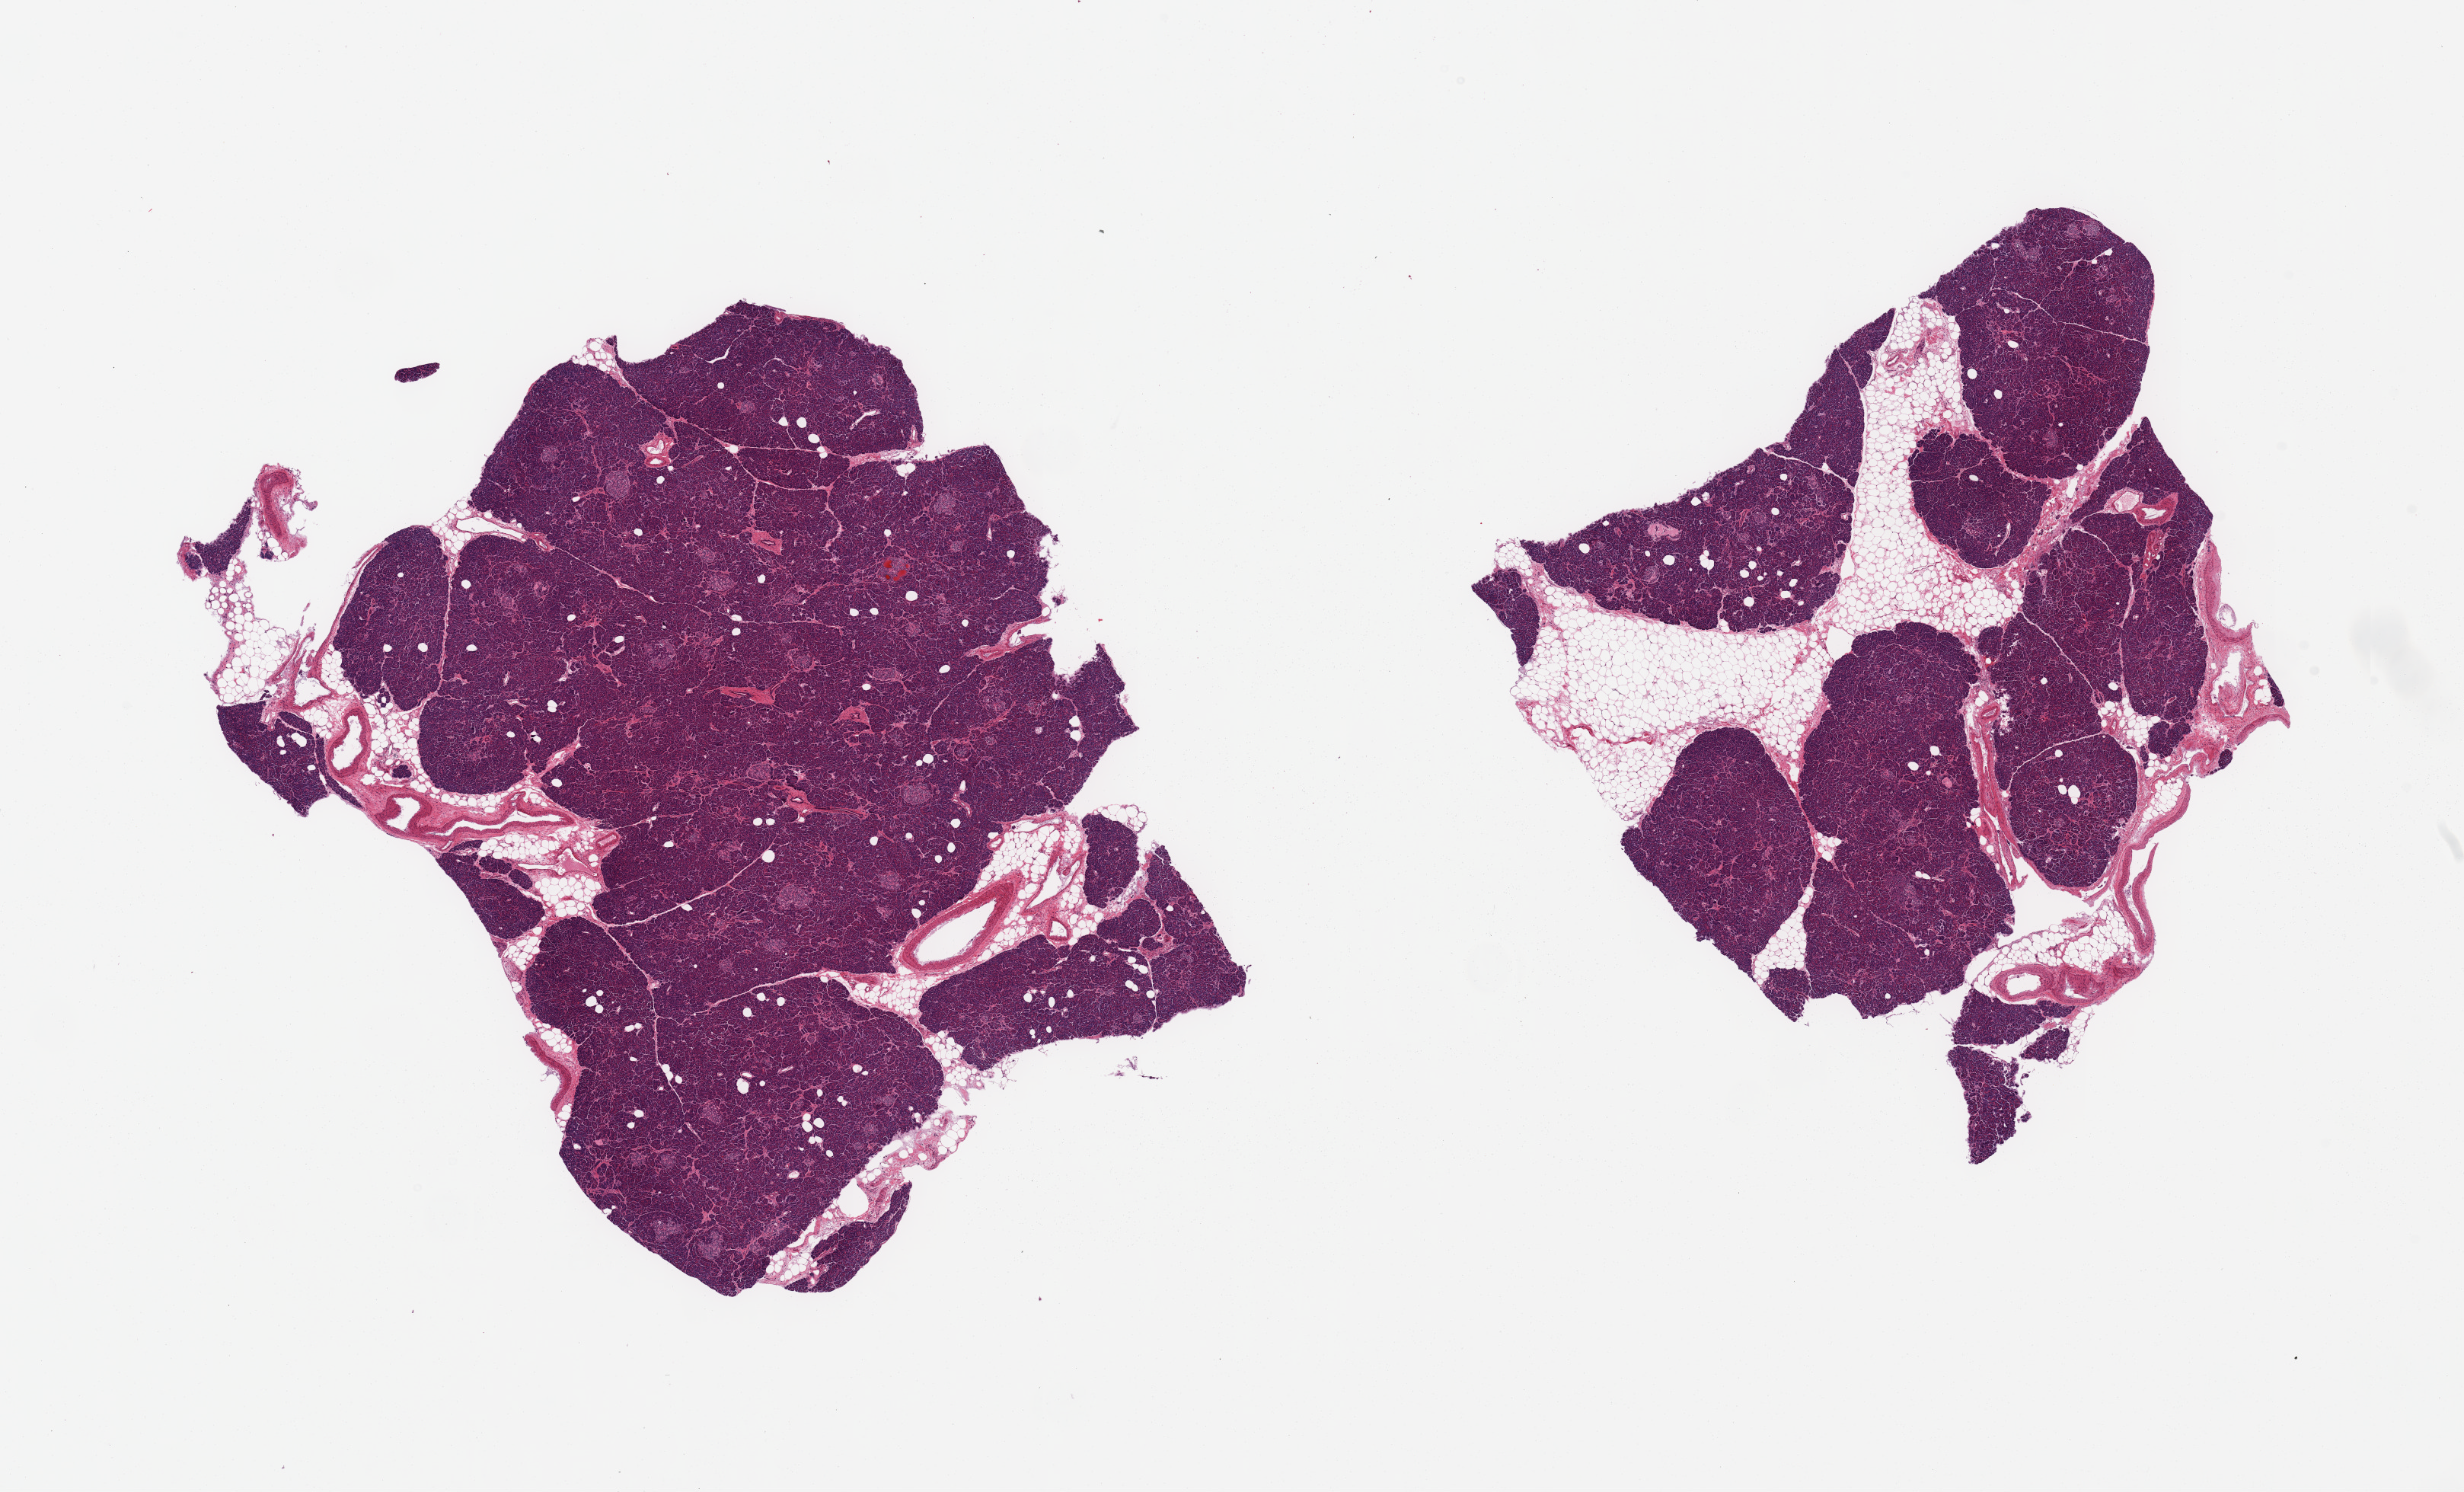
Whole-slide image, haematoxylin and eosin stain — shown as a low-resolution overview of the whole scanned area (about 25.6 x 15.5 mm), PAXgene-fixed, paraffin-embedded tissue, sampled site (target tissue): pancreas, donor tissue sample.
* reviewer comment on this tissue sample: 2 pieces; 10% & 30% internal fat; several partially sclerosed islets